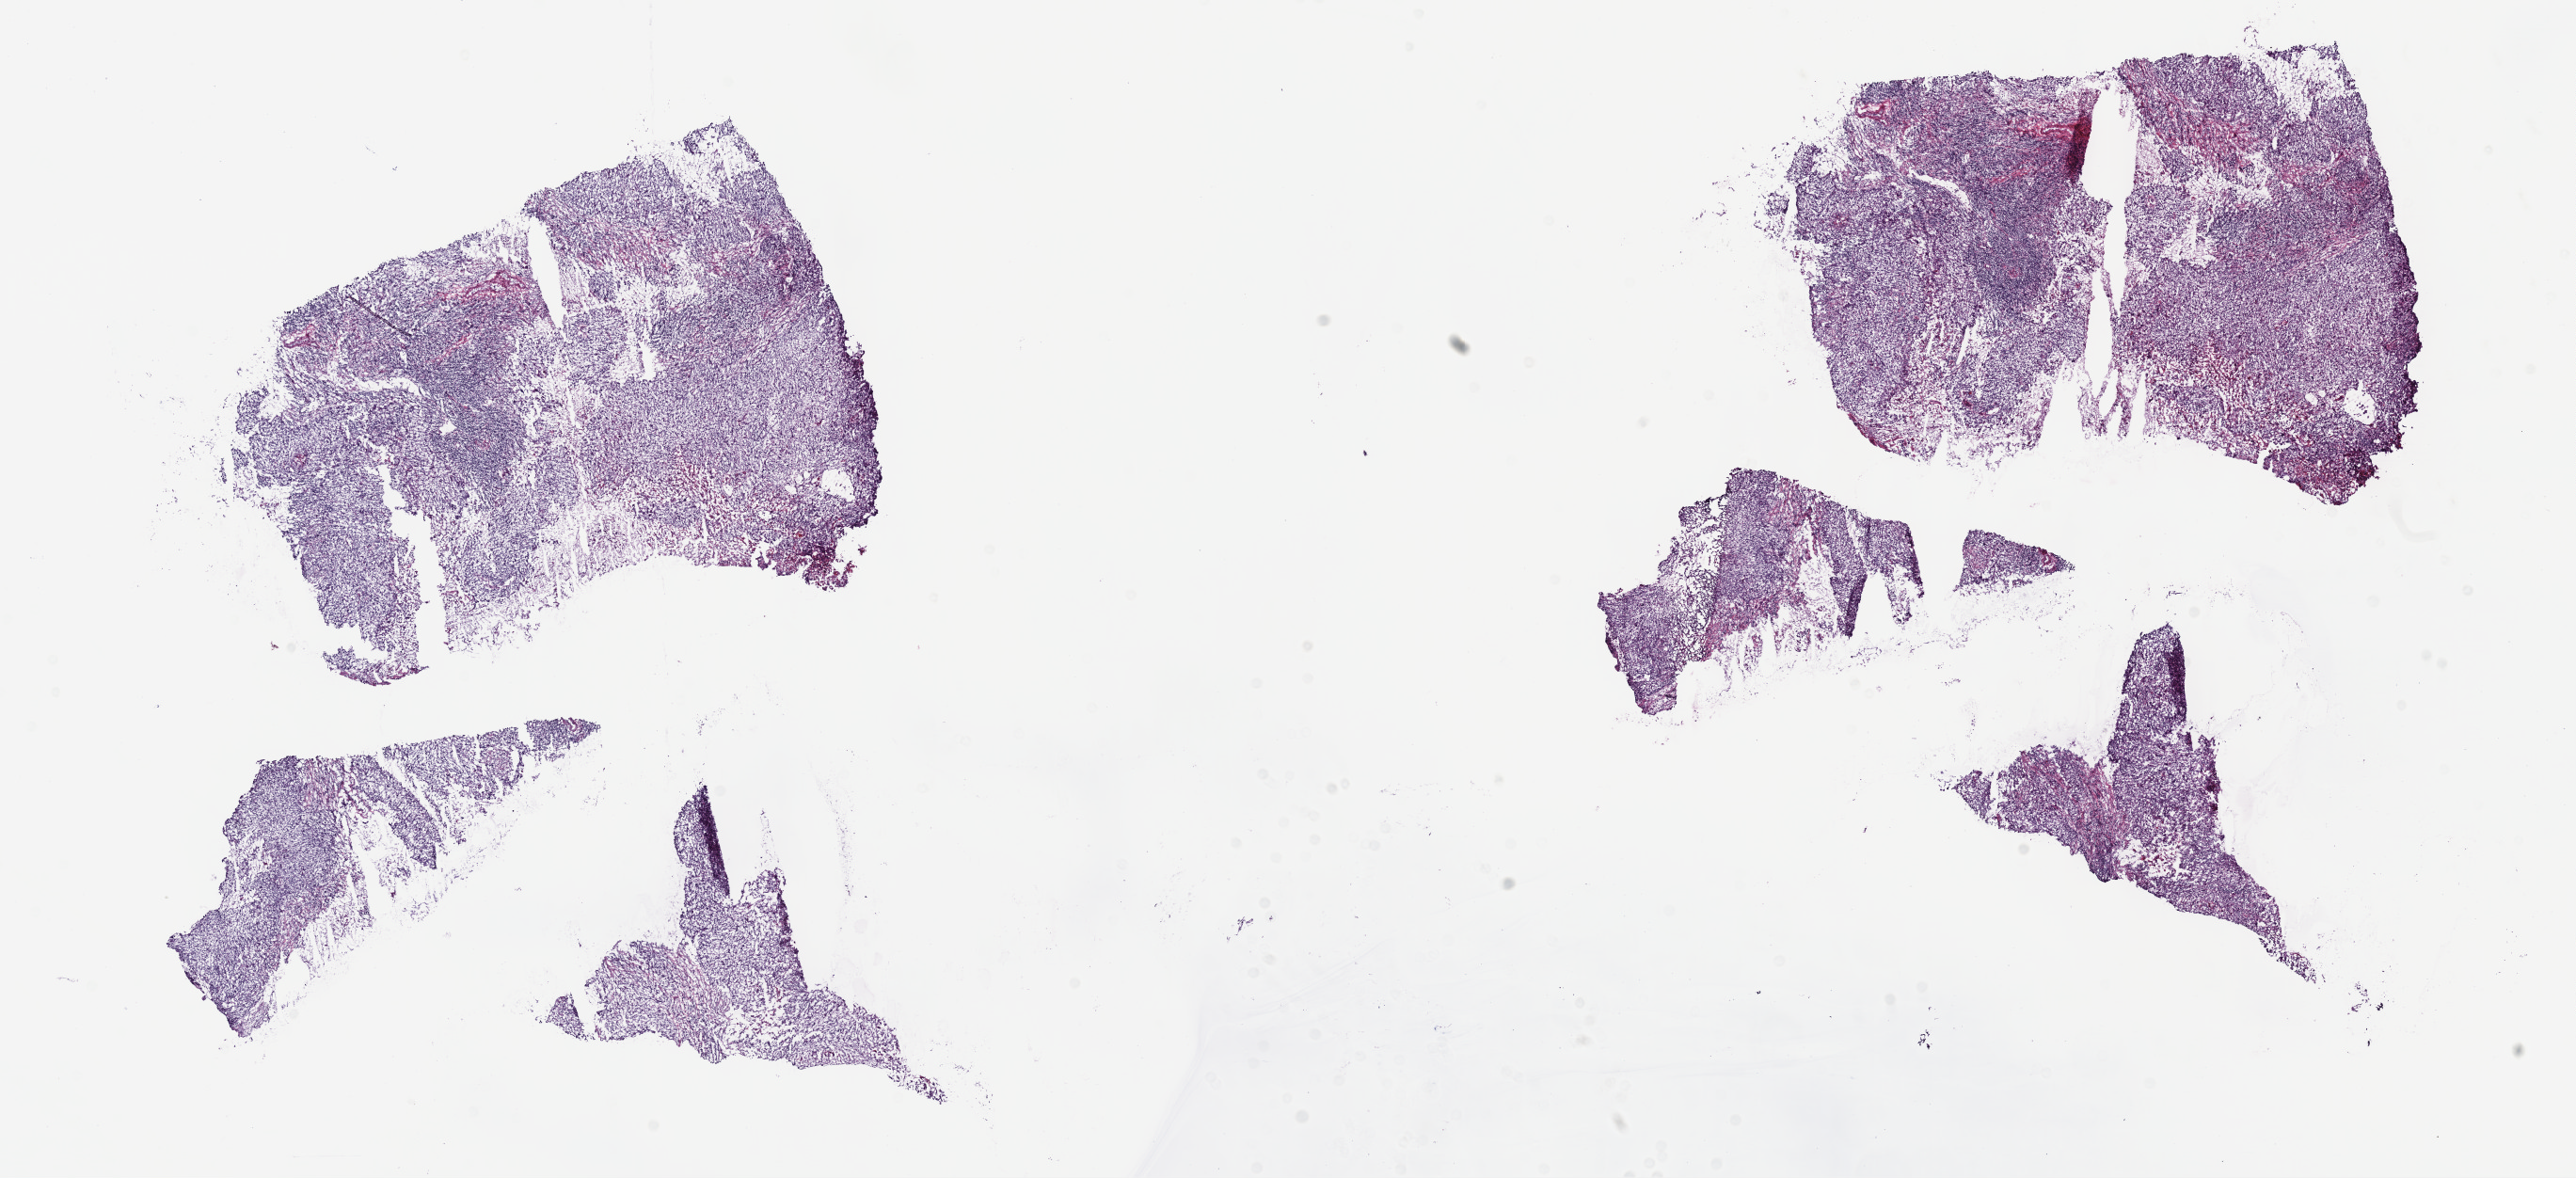
Whole-slide histology image, H&E, shown as a low-resolution overview of the whole scanned area (about 22.1 x 10.1 mm), frozen section, sample: primary tumour, cervix. Patient: female, age at initial diagnosis 38 years. Histologic grade: G3 (poorly differentiated). Slide review estimates, as recorded: tumour cells 80%, tumour nuclei 80%, normal cells 0%, stromal cells 10%, necrosis 10%. Infiltration values recorded for this section: lymphocyte infiltration 20%, monocyte infiltration 20%, neutrophil infiltration 40%.
Pathologic diagnosis: Squamous cell carcinoma, NOS (cervix uteri). FIGO stage: IIB.